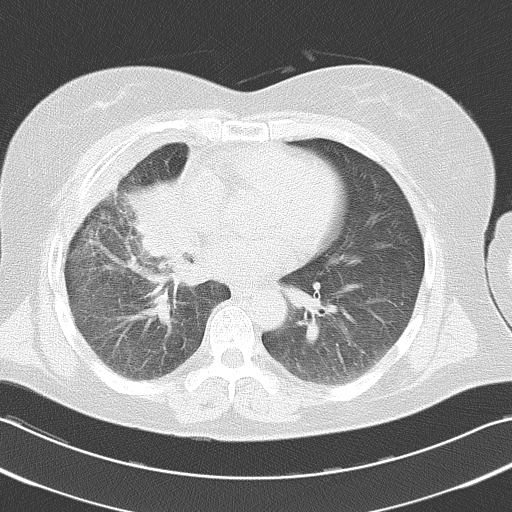
Chest CT, one axial slice. Slice 14 of 38 in the series (ordered by position). Reconstruction kernel B70f. Lung window (W 1500 / L -600 HU). 512 × 512 image matrix, field of view 346 × 346 mm. Patient: female, 52 years. Case-level facts recorded for this patient, not image findings: clinical TNM (as recorded): T3 N1 M0.
Structures marked on this image (rectangle marked by the reading radiologist):
- lung tumour (recorded histology: squamous cell carcinoma): box from (x=116, y=169) to (x=195, y=288) px